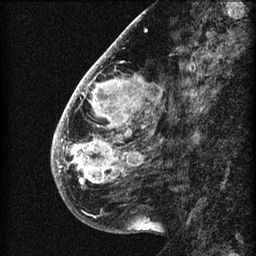
Breast MRI (dynamic contrast-enhanced), one sagittal slice; slice 21 of 60 in the series (ordered by position); 3 images stored at this slice position (order not interpretable as contrast timing); 1.5 T; TE 4.2 ms, TR 22.7 ms; 2 mm slice thickness; 256 × 256 image matrix. Patient: female, 48 years. From the clinical record (not read from this slice): setting: breast cancer imaged before/during neoadjuvant chemotherapy; receptor status: triple-negative.
Annotated regions visible in this slice (semi-automatically segmented with operator editing):
- analysis volume of interest (the breast-tissue region the enhancement analysis was run in; not a lesion): bounding box (x1, y1, x2, y2) in pixels: (51, 30, 173, 207)
- tumour enhancement mask (voxels above the 90 % enhancement threshold inside the analysis volume of interest): (52, 60, 141, 186)